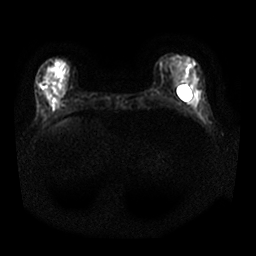
Breast MRI, one axial slice; position 8 of 25 along the scan axis; diffusion-weighted series; image 2 of 4 stored at this slice position (different b-values; order by instance number); 1.5 T; 256 × 256 image matrix, field of view 340 × 340 mm. Female patient.
Annotated regions visible in this slice (outlined manually by an expert reader):
- tumour on diffusion-weighted imaging: bounding box (x1, y1, x2, y2) in pixels: (39, 84, 43, 88)